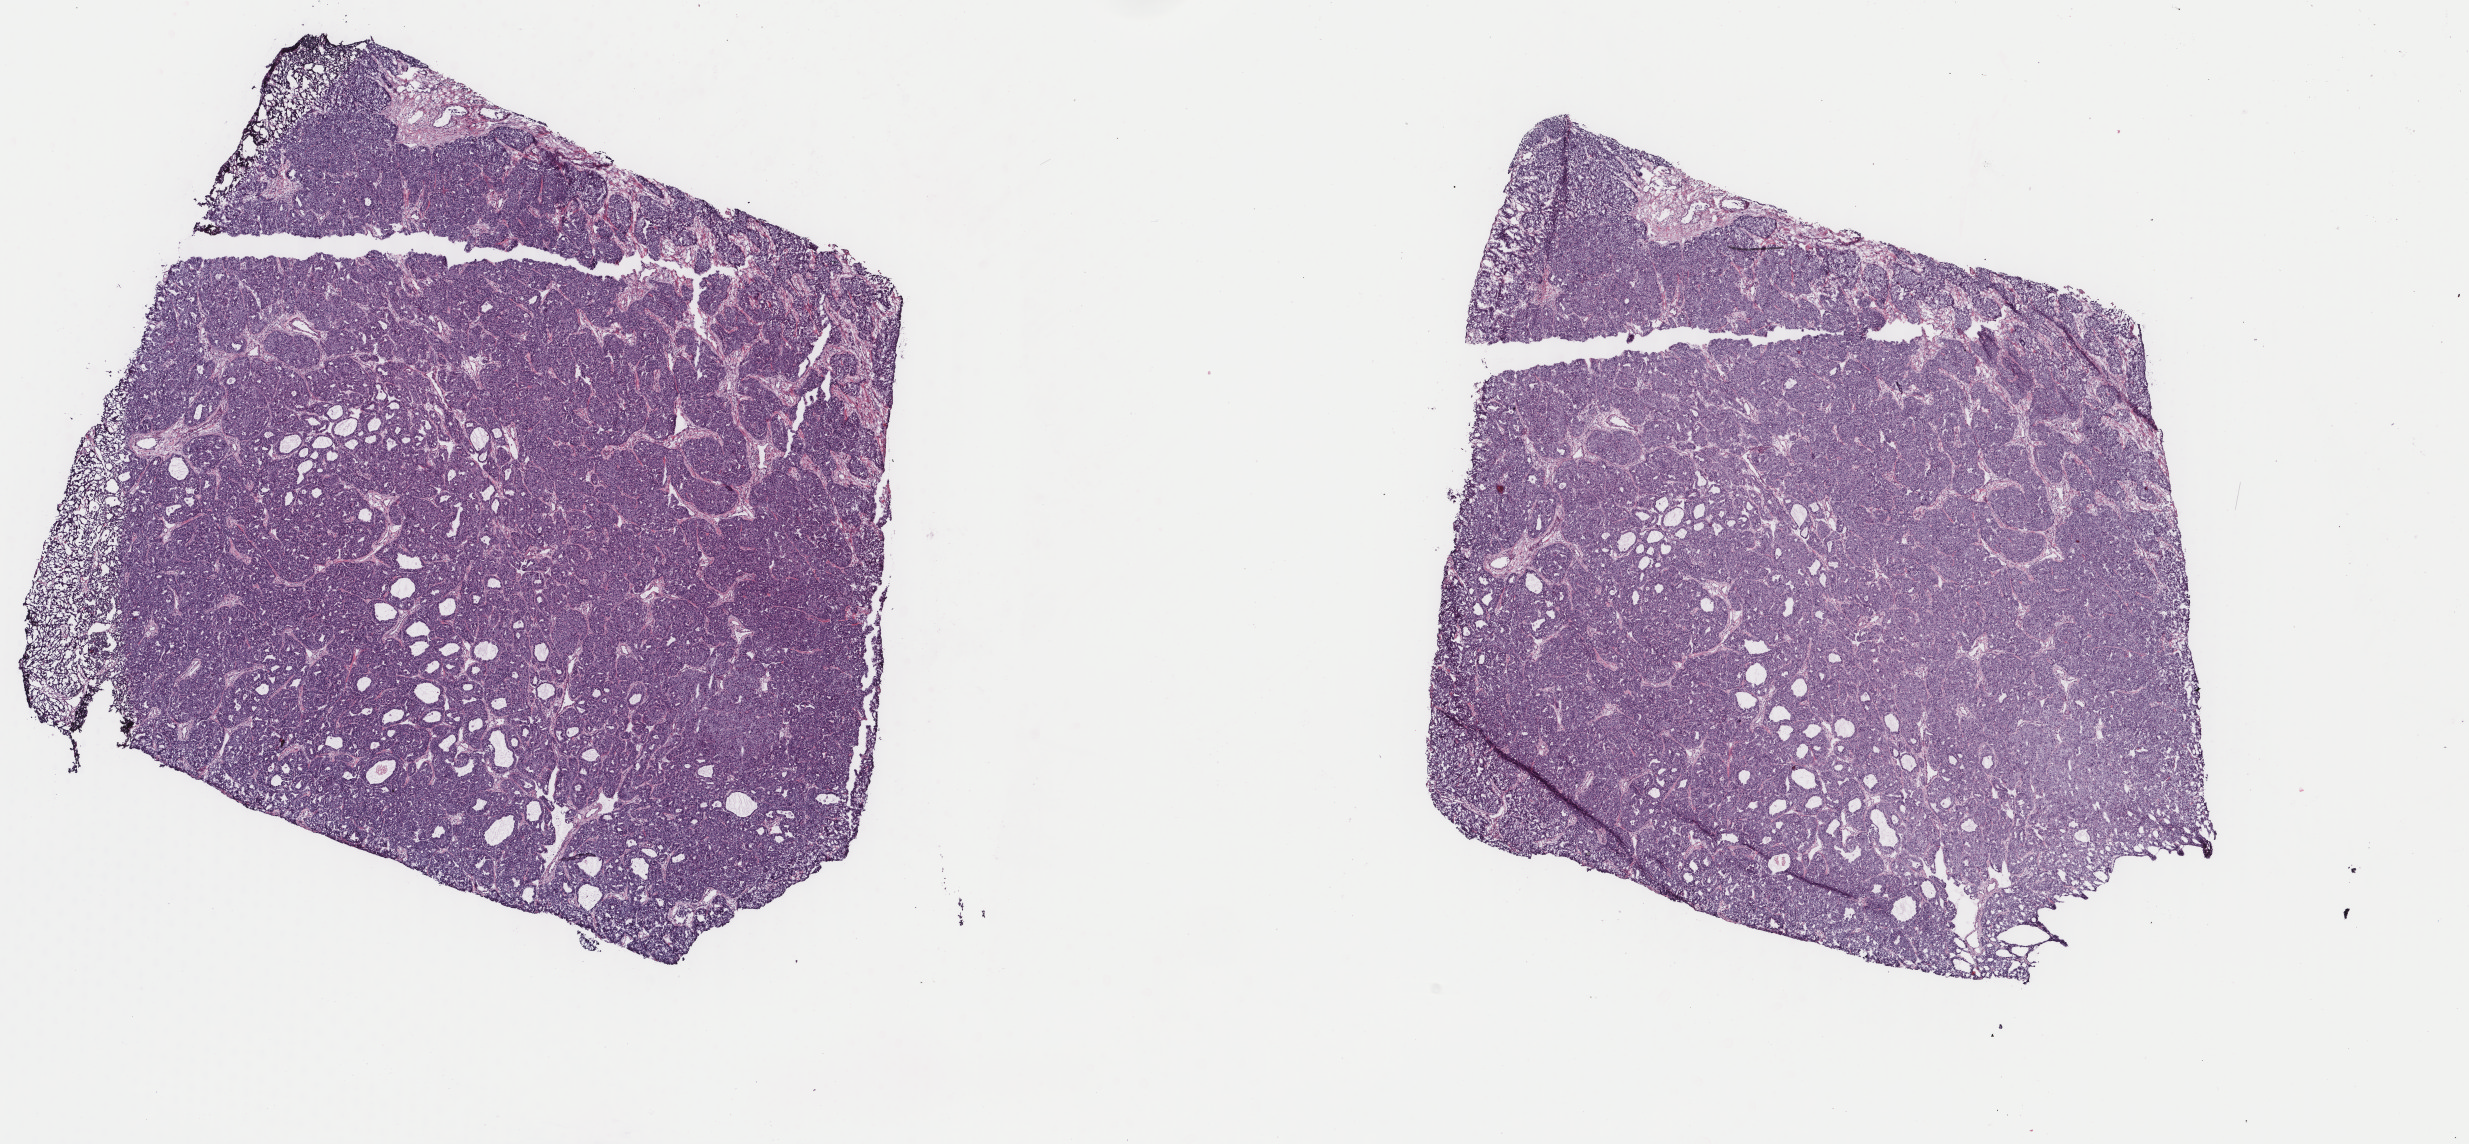
Hematoxylin and eosin (H&E) stained whole-slide image, whole scanned area (about 19.6 x 9.1 mm, acquisition: 40x scan) shown as a low-resolution overview, frozen section from the top of the tissue portion, primary tumour sample from the liver. Patient: female, age at initial diagnosis 56 years. Histologic grade: G3 (poorly differentiated). Composition of this section per pathologist review: tumour cells 100%, tumour nuclei 80%, normal cells 0%, stromal cells 0%, necrosis 0%. Infiltration values recorded for this section: lymphocyte infiltration 2%, monocyte infiltration 0%, neutrophil infiltration 0%.
* diagnosis: Hepatocellular carcinoma, NOS
* AJCC pathologic stage: I (6th edition)
* TNM: T1 N0 M0